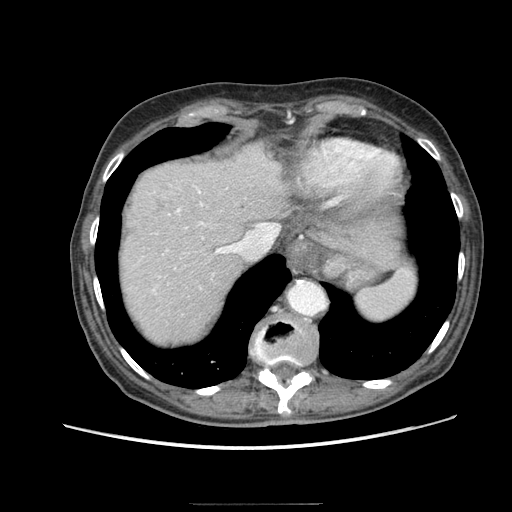
Contrast-enhanced abdominal CT (liver protocol), one axial slice; position 70 of 83 along the scan axis; reconstruction kernel STANDARD; soft-tissue window (W 400 / L 40 HU); 2.5 mm slice thickness; 512 × 512 image matrix, field of view 360 × 360 mm. From the clinical record (not read from this slice): diagnosis: hepatocellular carcinoma (patient treated with transarterial chemoembolisation; whether this scan precedes or follows treatment is not stated here); TNM stage (as recorded): Stage-I; Child-Pugh class: A; tumour differentiation: moderately differentiated; tumour nodularity: uninodular.
Annotated regions visible in this slice (semi-automatic segmentation, software-assisted and operator-edited):
- abdominal aorta: box from (x=288, y=282) to (x=327, y=315) px
- liver parenchyma outside the tumour (the mass and vessels are separate outlines, so this box may not span the whole liver): (x=122, y=143)–(x=288, y=342)
- liver vessels: (x=153, y=185)–(x=236, y=291)